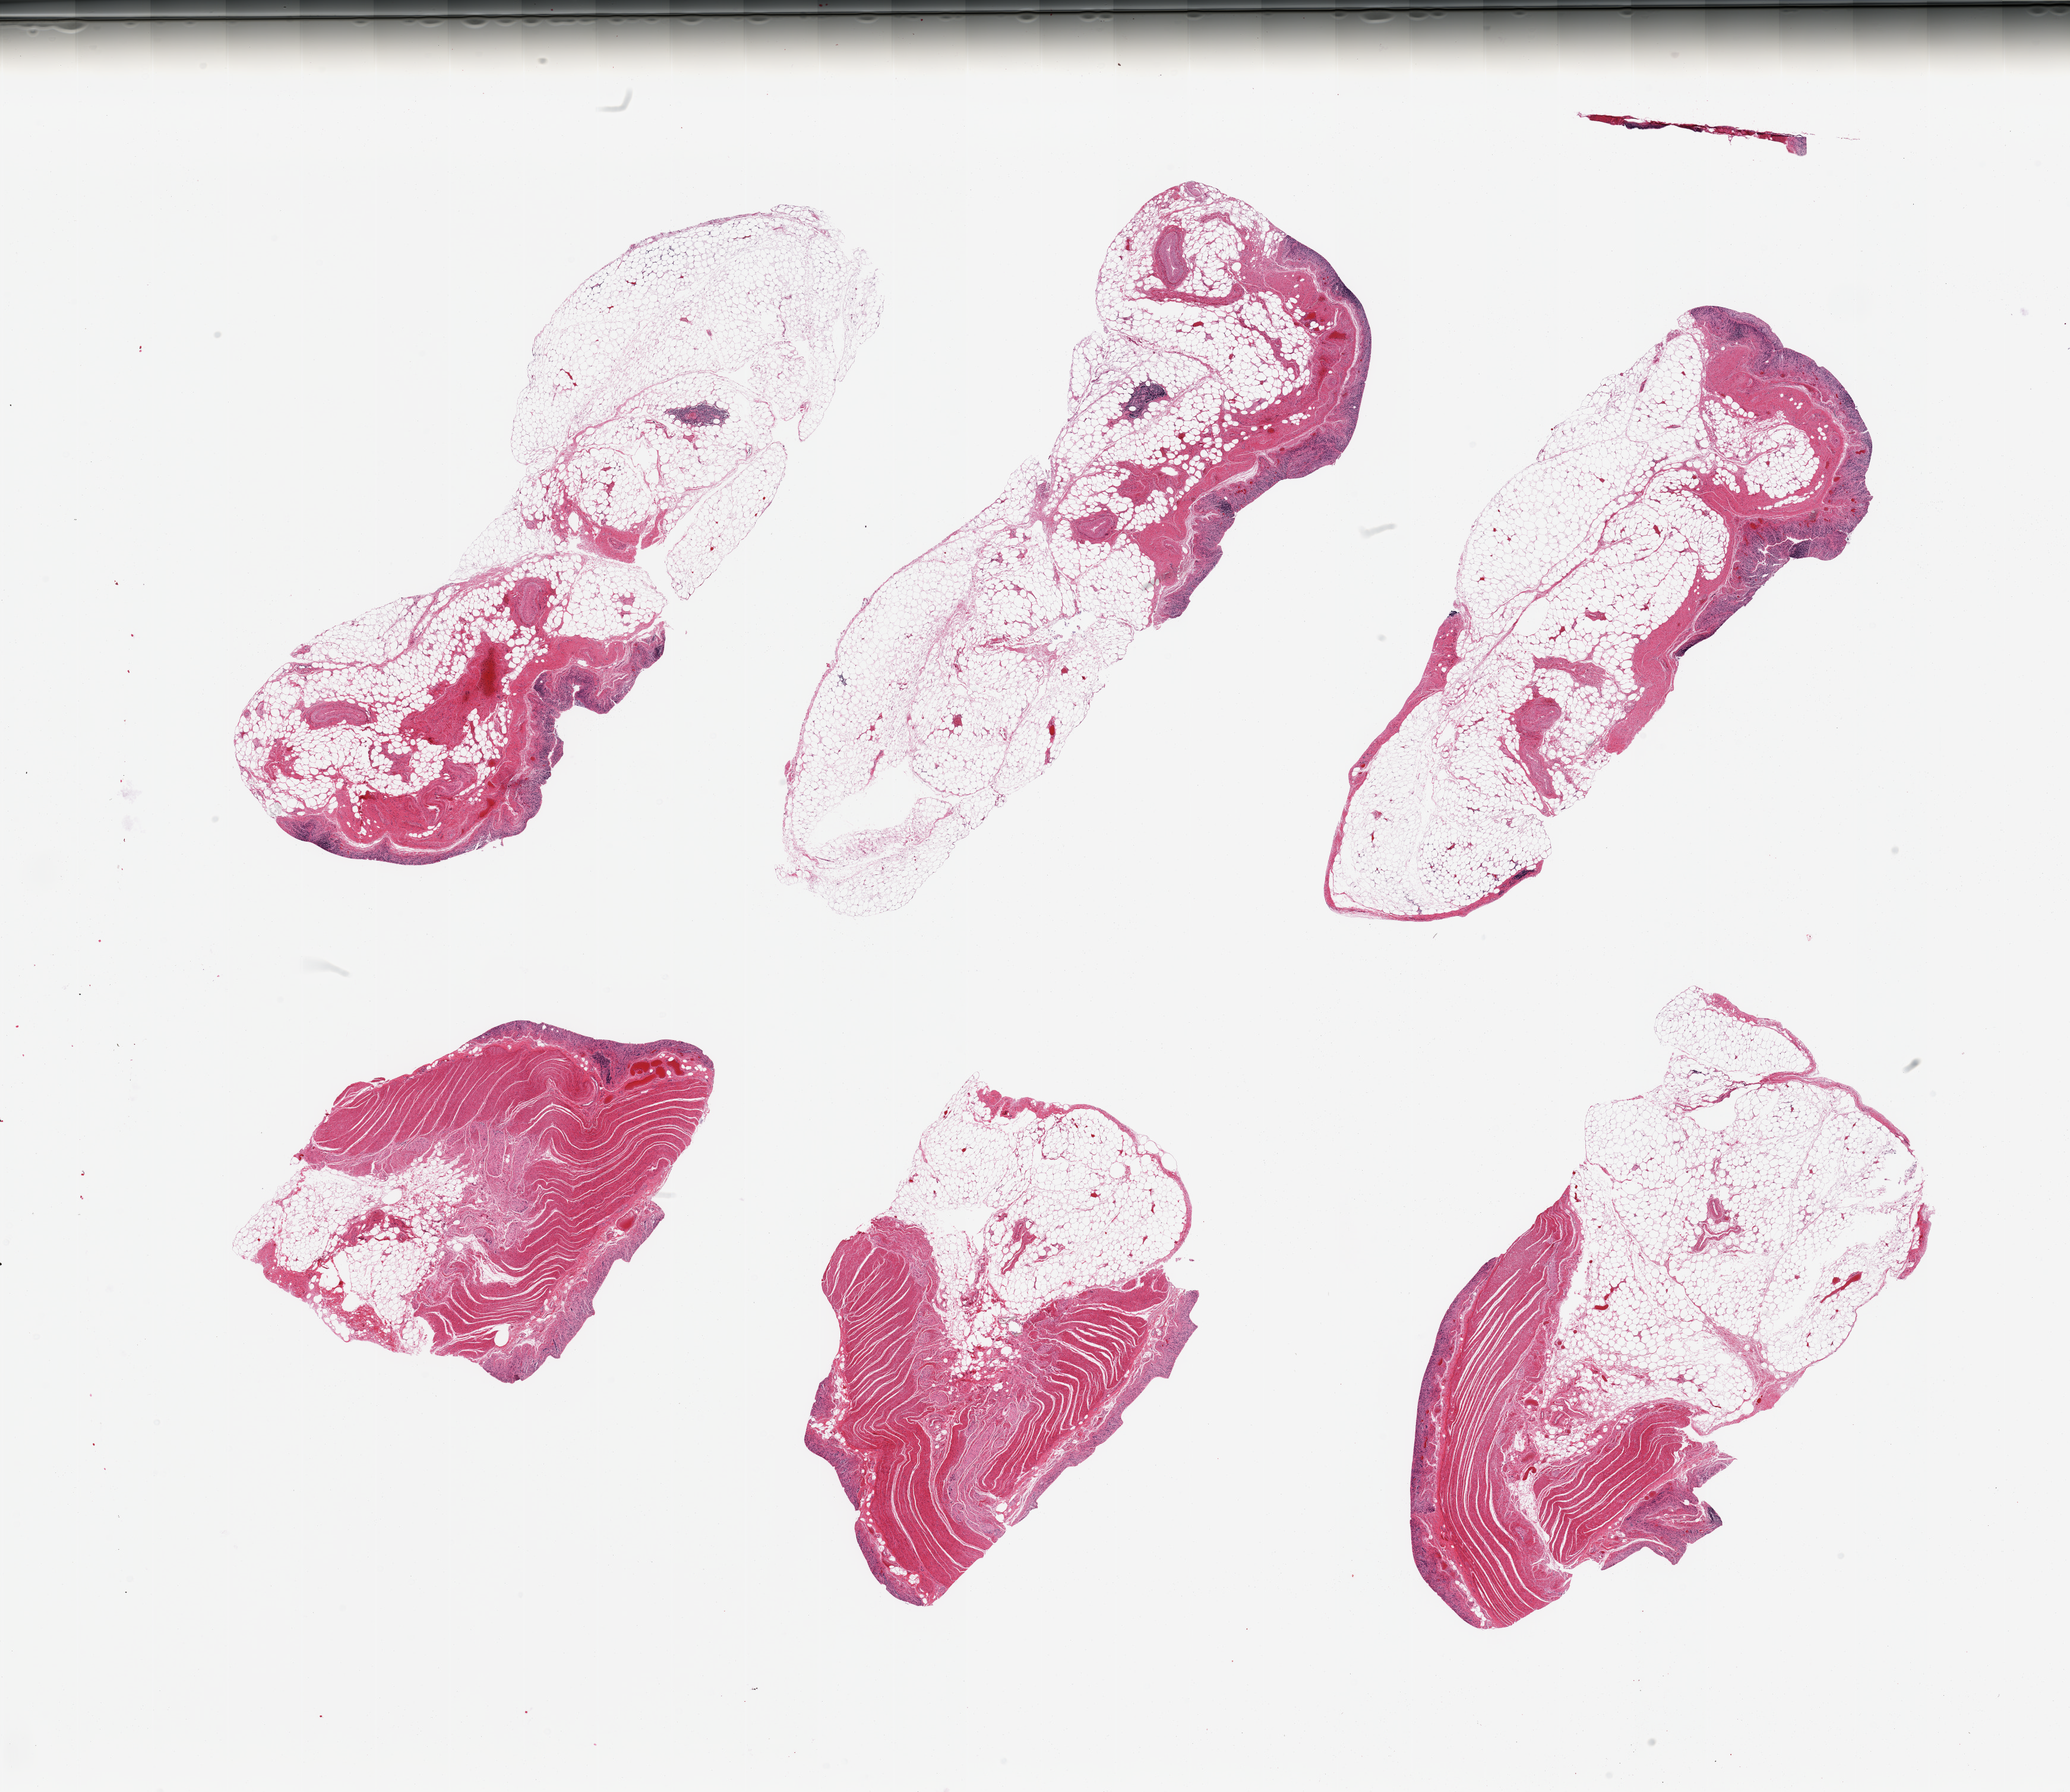
Whole-slide image, haematoxylin and eosin stain, a low-resolution overview of the entire scanned area, about 27.6 x 23.9 mm (acquisition: 20x scan); PAXgene-fixed, paraffin-embedded tissue; sampled site (target tissue): sigmoid colon; tissue donor sample.
• pathologist's review note for this sample: 6 pieces, ~60-70% fat, rest is target muscularis